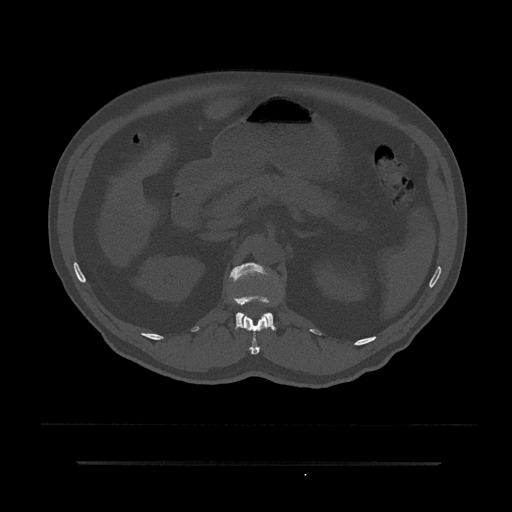
CT including the spine, one axial slice. Slice 178 of 797 in the series (ordered by position). Reconstruction kernel Br40s/3. Bone window (W 1800 / L 400 HU). 512 × 512 image matrix, field of view 464 × 464 mm. Patient: male, 59 years. From the clinical record (not read from this slice): primary cancer: bile ducts; vertebrae with lytic lesions (as recorded): T10.
Outlined on this slice (semi-automatically segmented with operator editing):
- L1 vertebra: bounding box (x1, y1, x2, y2) in pixels: (230, 263, 276, 331)
- T12 vertebra: (241, 314, 270, 355)